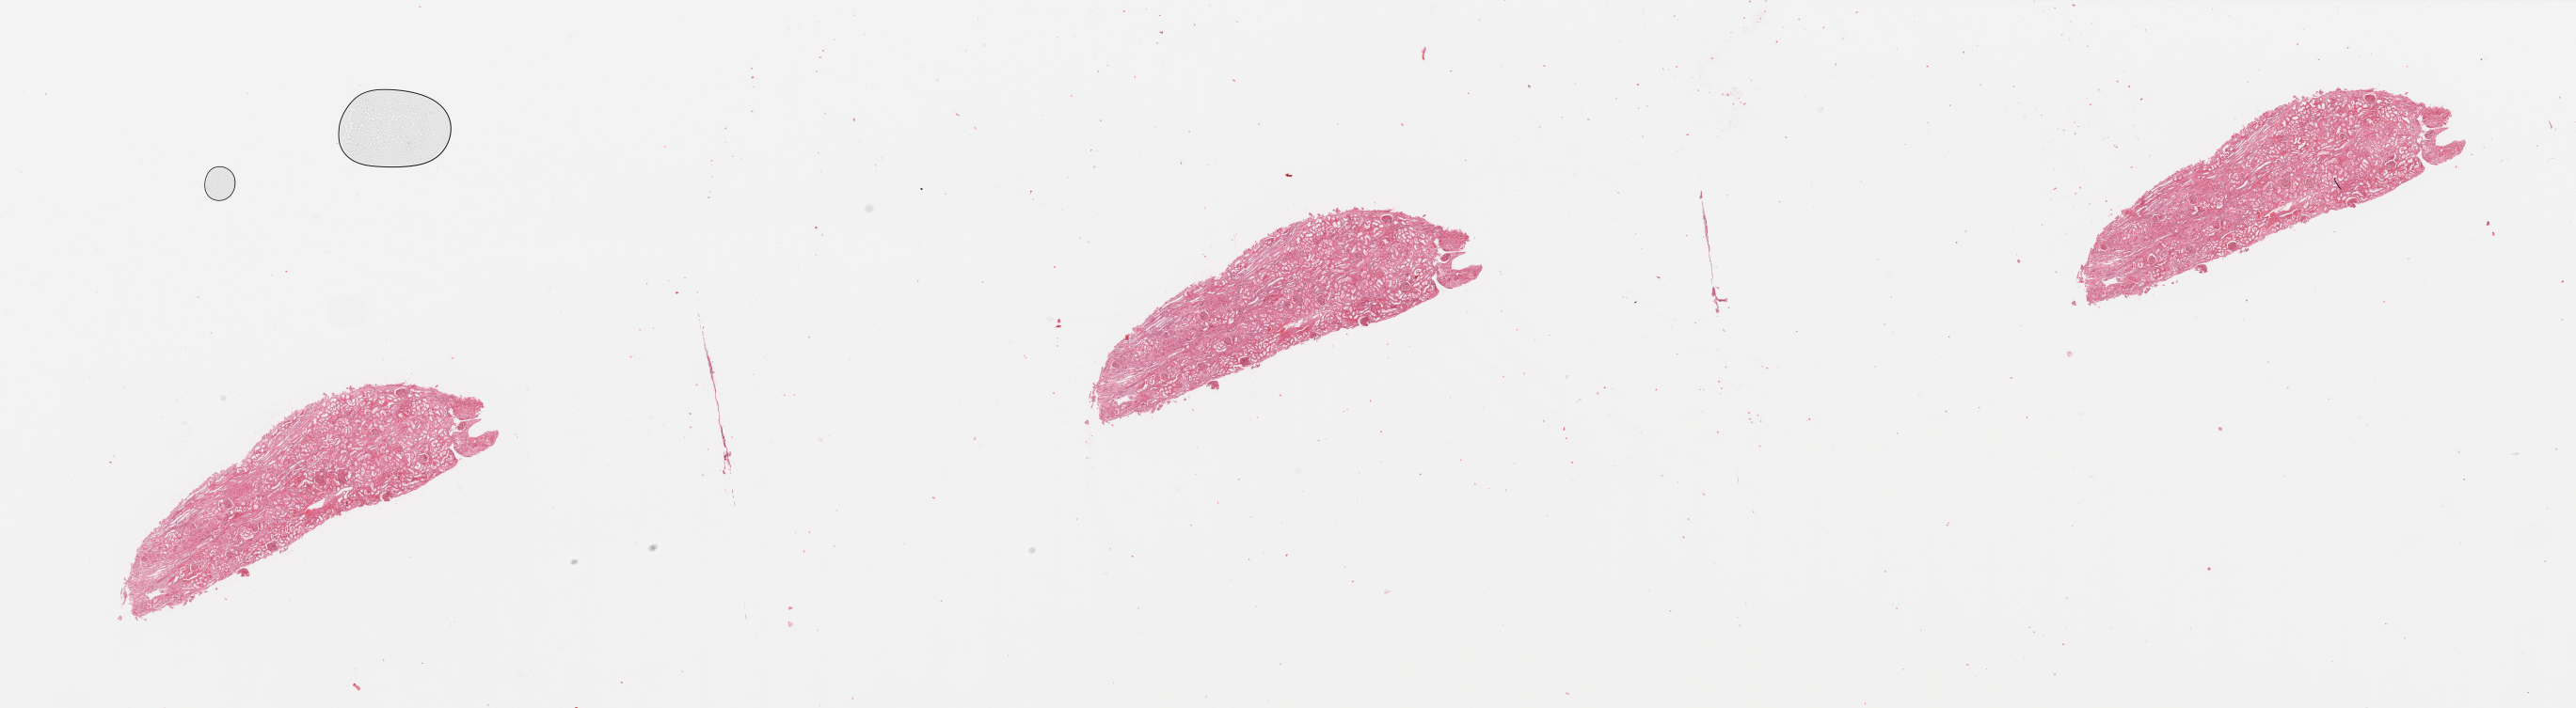
Hematoxylin and eosin (H&E) stained whole-slide image — whole scanned area (about 43.3 x 11.9 mm) shown as a low-resolution overview; kidney, normal (non-tumour) tissue. Patient: male, age 47 years.
This section: normal (non-tumour) tissue from the same patient. Patient diagnosis: Renal cell carcinoma, NOS.